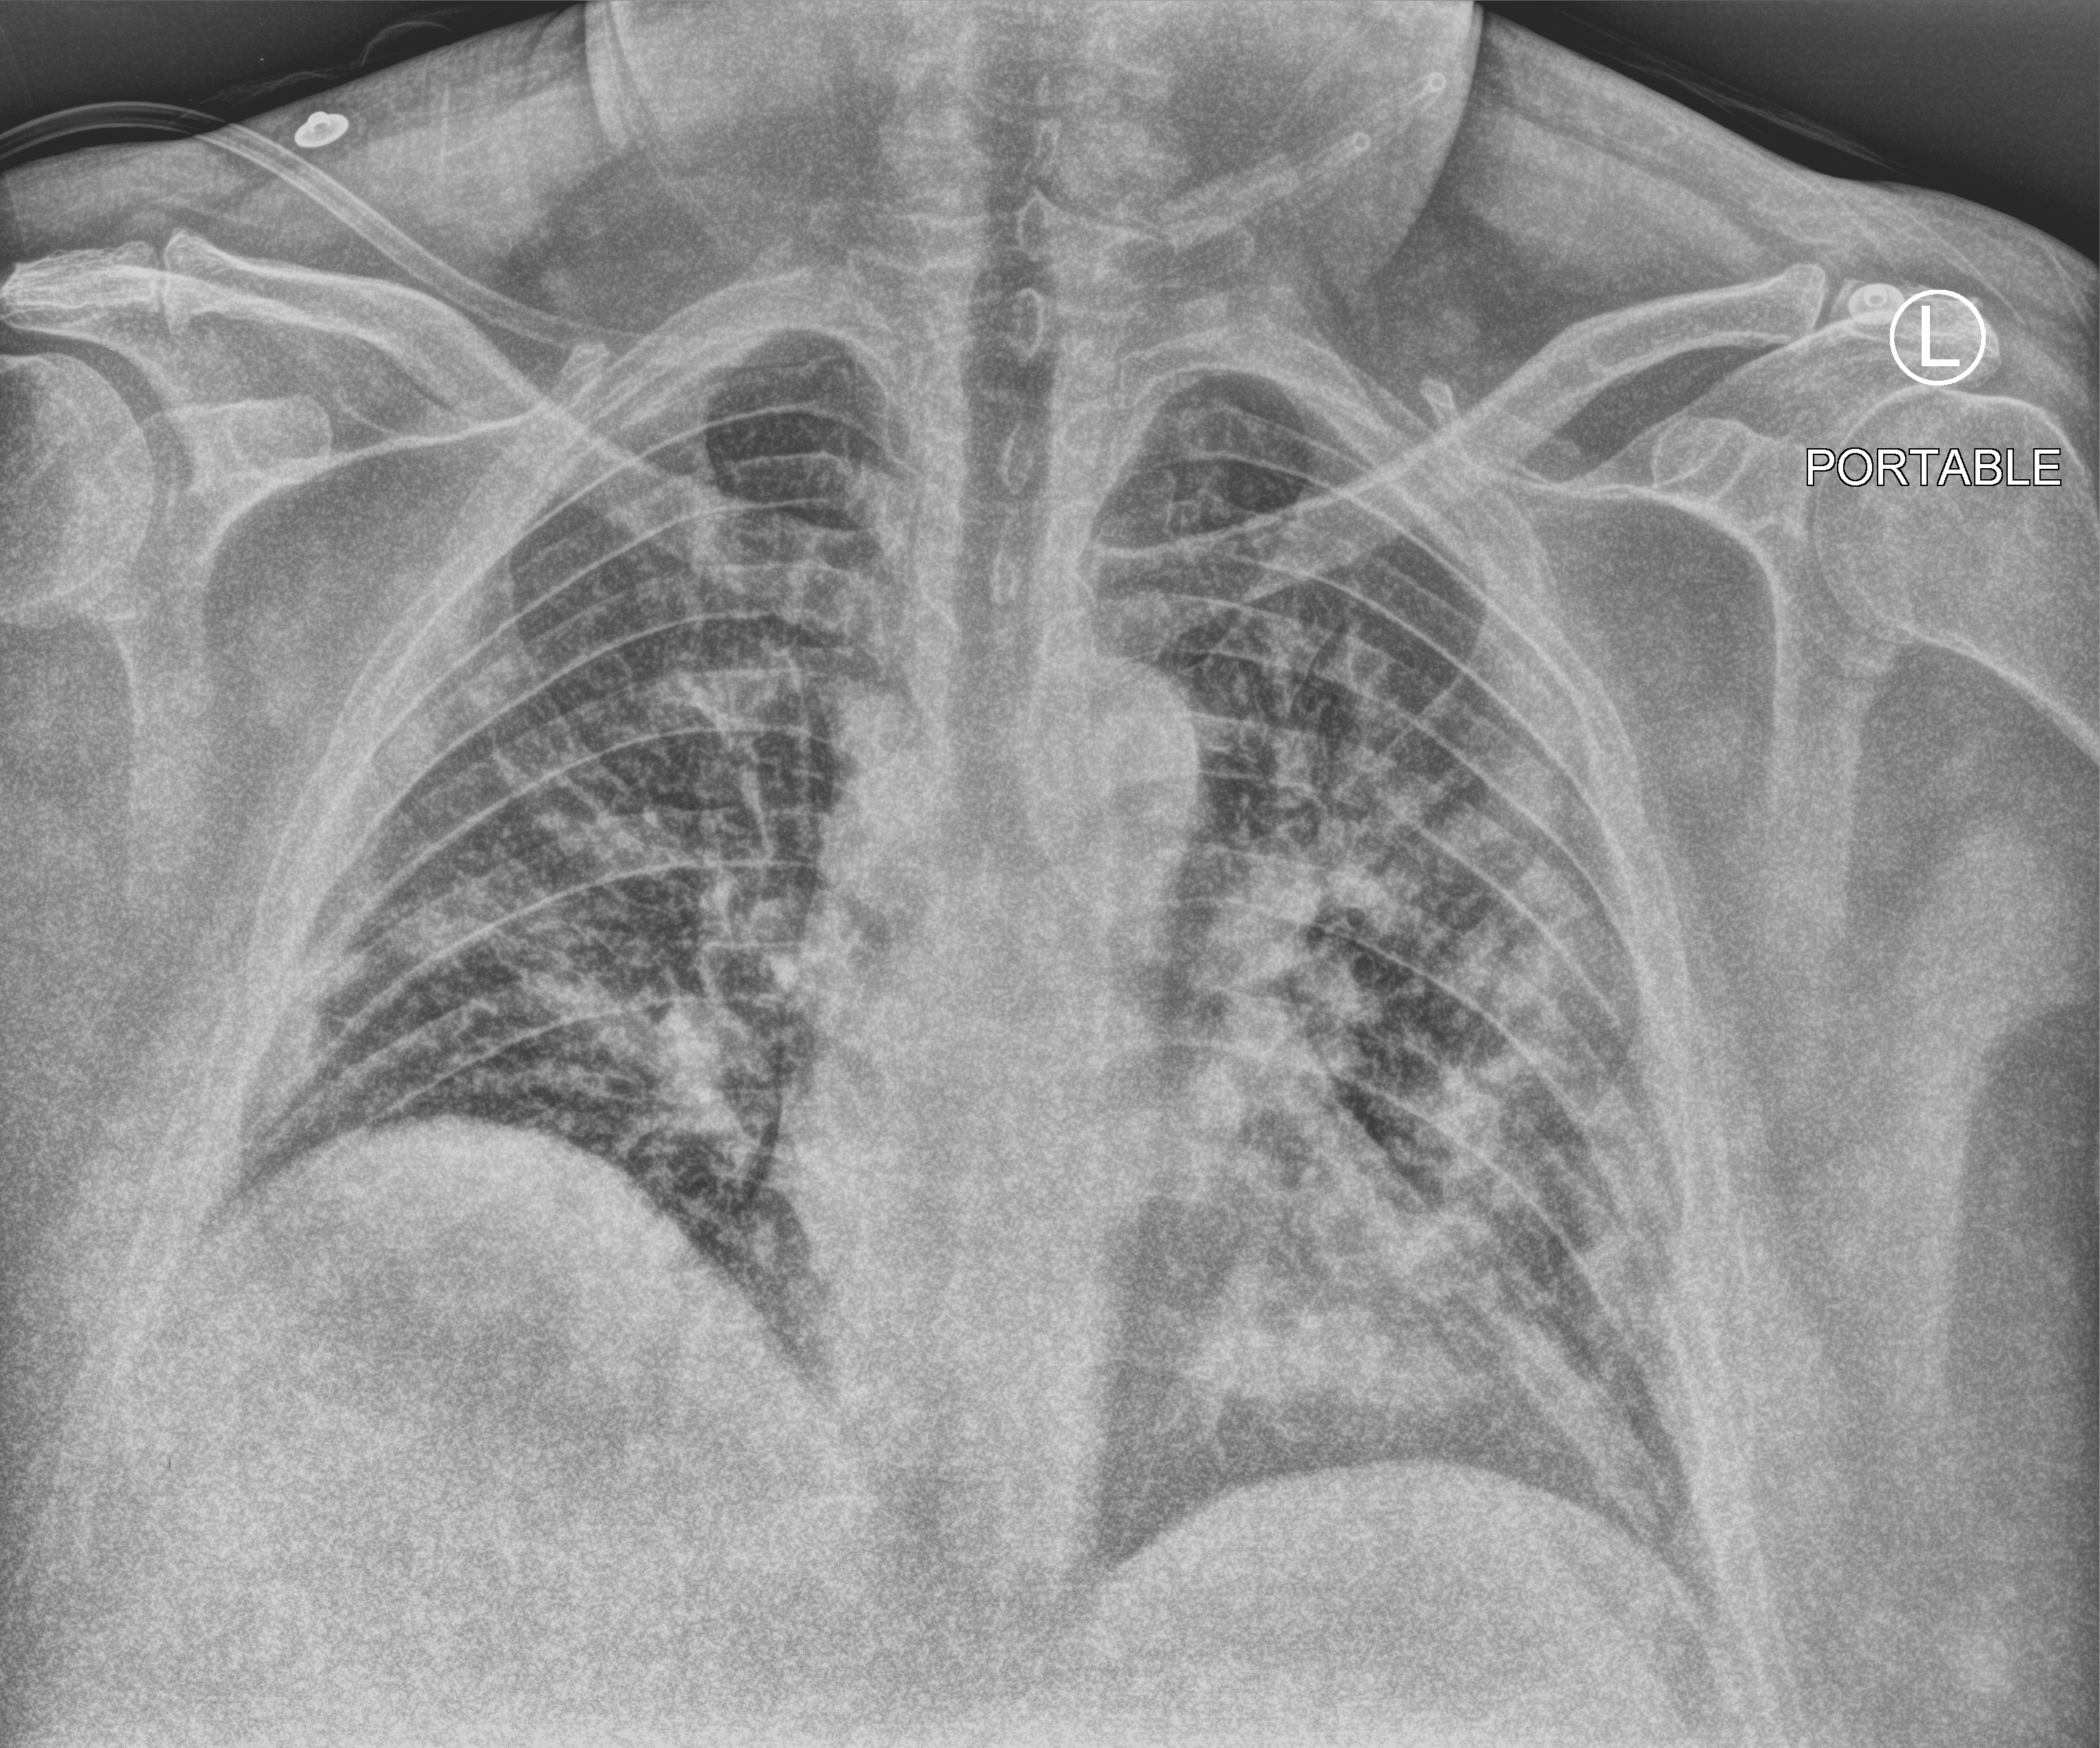
Portable chest radiograph, anteroposterior (AP) projection. Patient hospitalised with COVID-19; male, aged 18–59 years.
From the hospital-stay record, not from the radiograph (when in the stay this image was taken is not recorded):
- length of hospital stay: 12 days
- hypertension (admission record): yes
- mechanically ventilated during this hospital stay: no